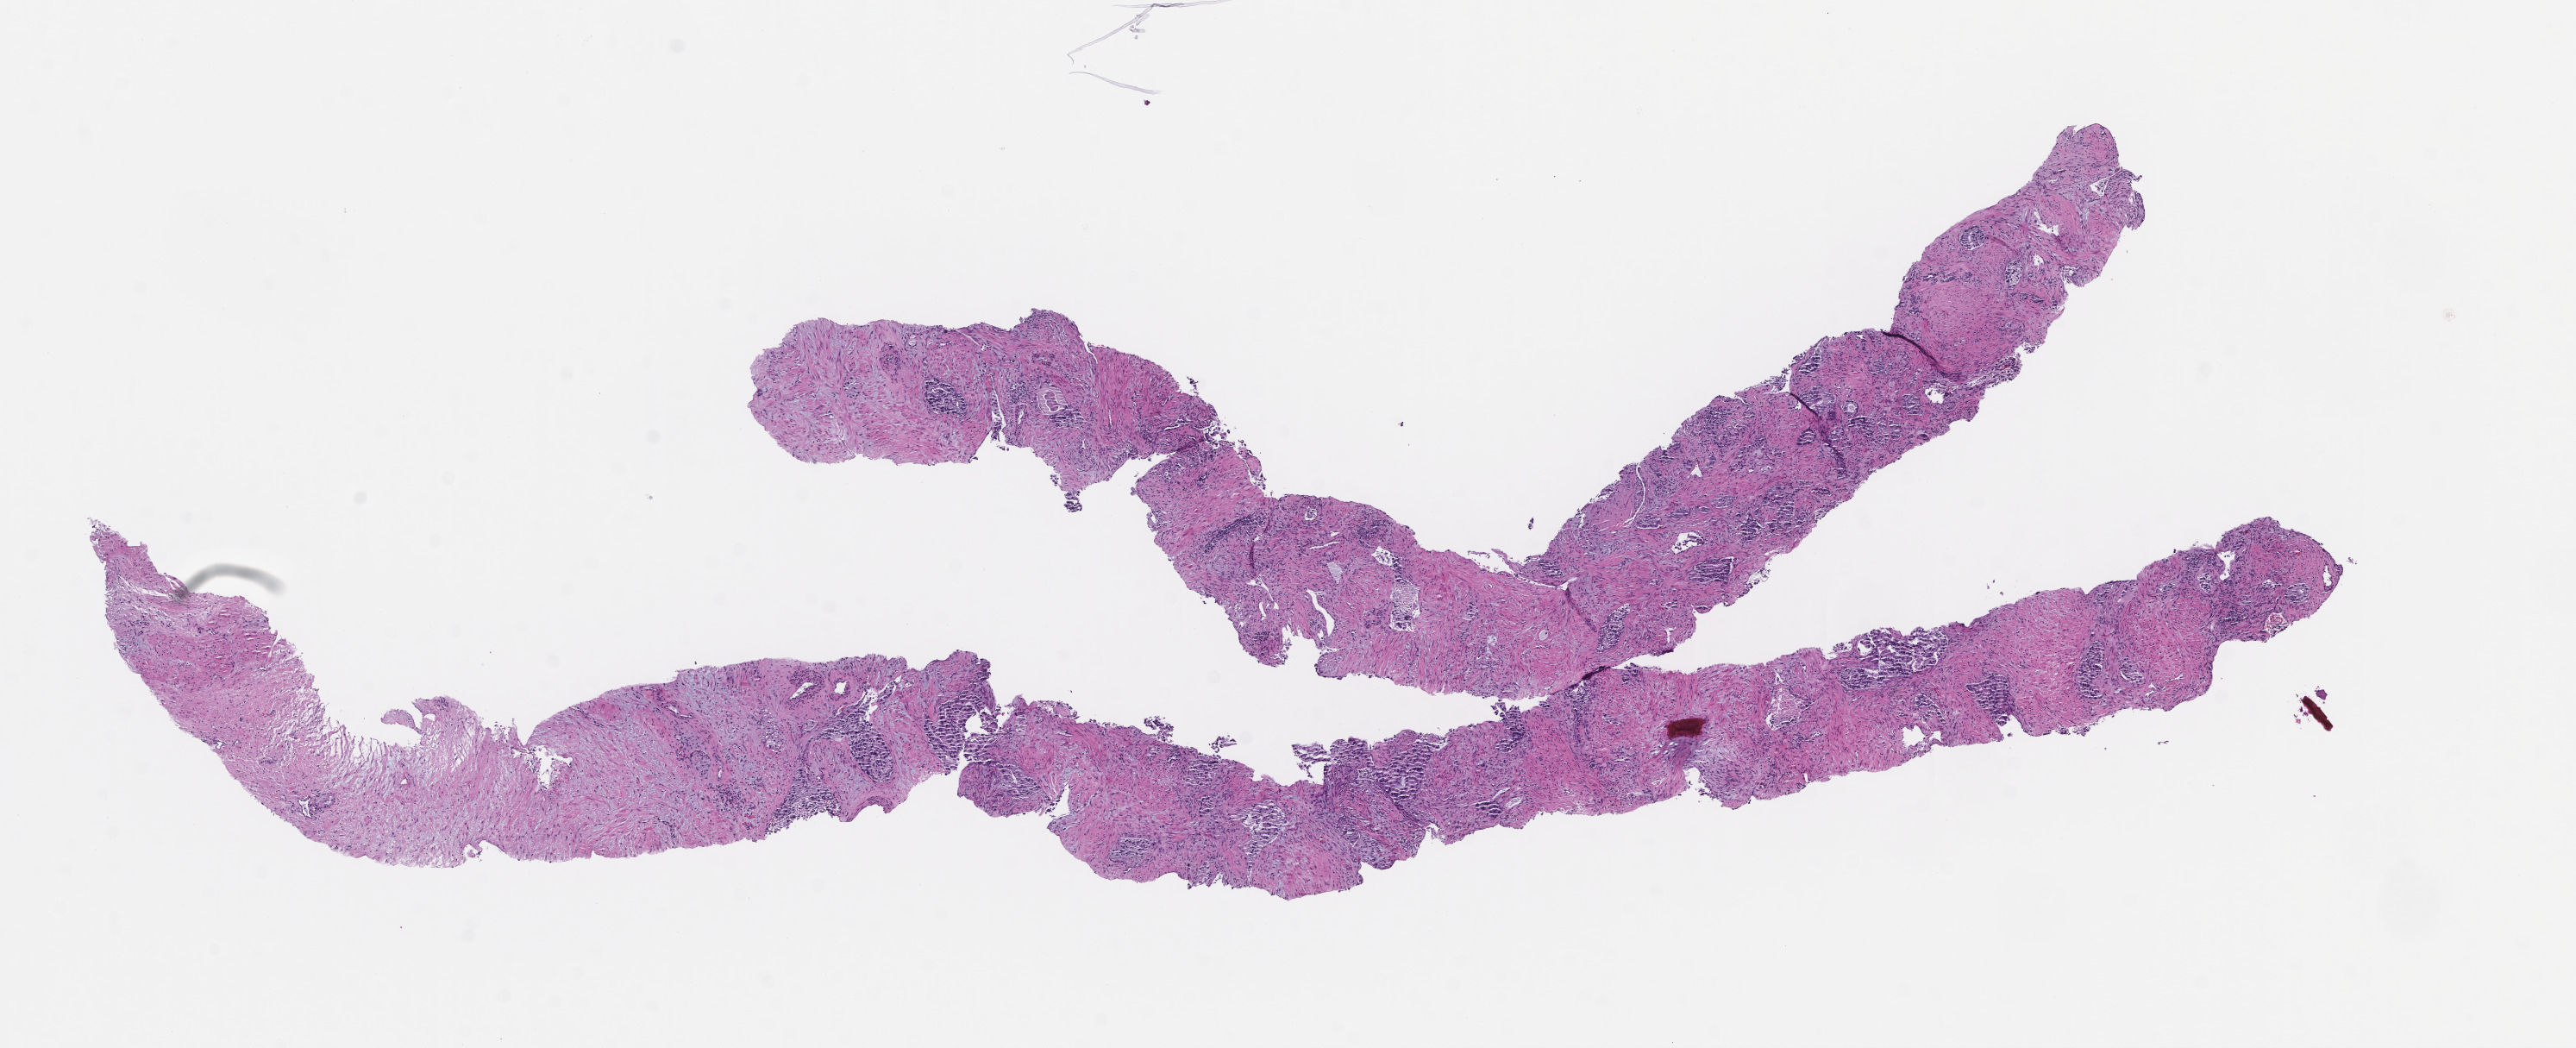
Whole-slide image, haematoxylin and eosin stain — low-resolution overview of the scanned area, about 12.1 x 4.9 mm, formalin-fixed paraffin-embedded section, tissue site: prostate. Patient: male.
- this section: primary tumor
- diagnosis: Prostate Carcinoma